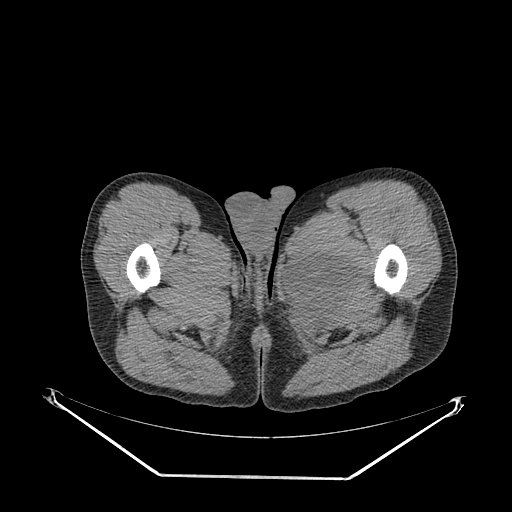
CT of an extremity soft-tissue mass (from a PET/CT study), one axial slice; slice 40 of 267 in the series (ordered by position); soft-tissue window (W 400 / L 40 HU); 3.75 mm slice thickness; 512 × 512 image matrix, field of view 500 × 500 mm. Male patient. Case-level facts recorded for this patient, not image findings: histological type: pleiomorphic liposarcoma; grade: high; site of the primary tumour: left thigh.
Outlined on this slice (expert contour drawn on MRI and transferred to this co-registered scan by the dataset authors):
- gross tumour volume including surrounding oedema: box from (x=286, y=247) to (x=357, y=325) px
- gross tumour volume (mass): (x=288, y=256)–(x=348, y=309)